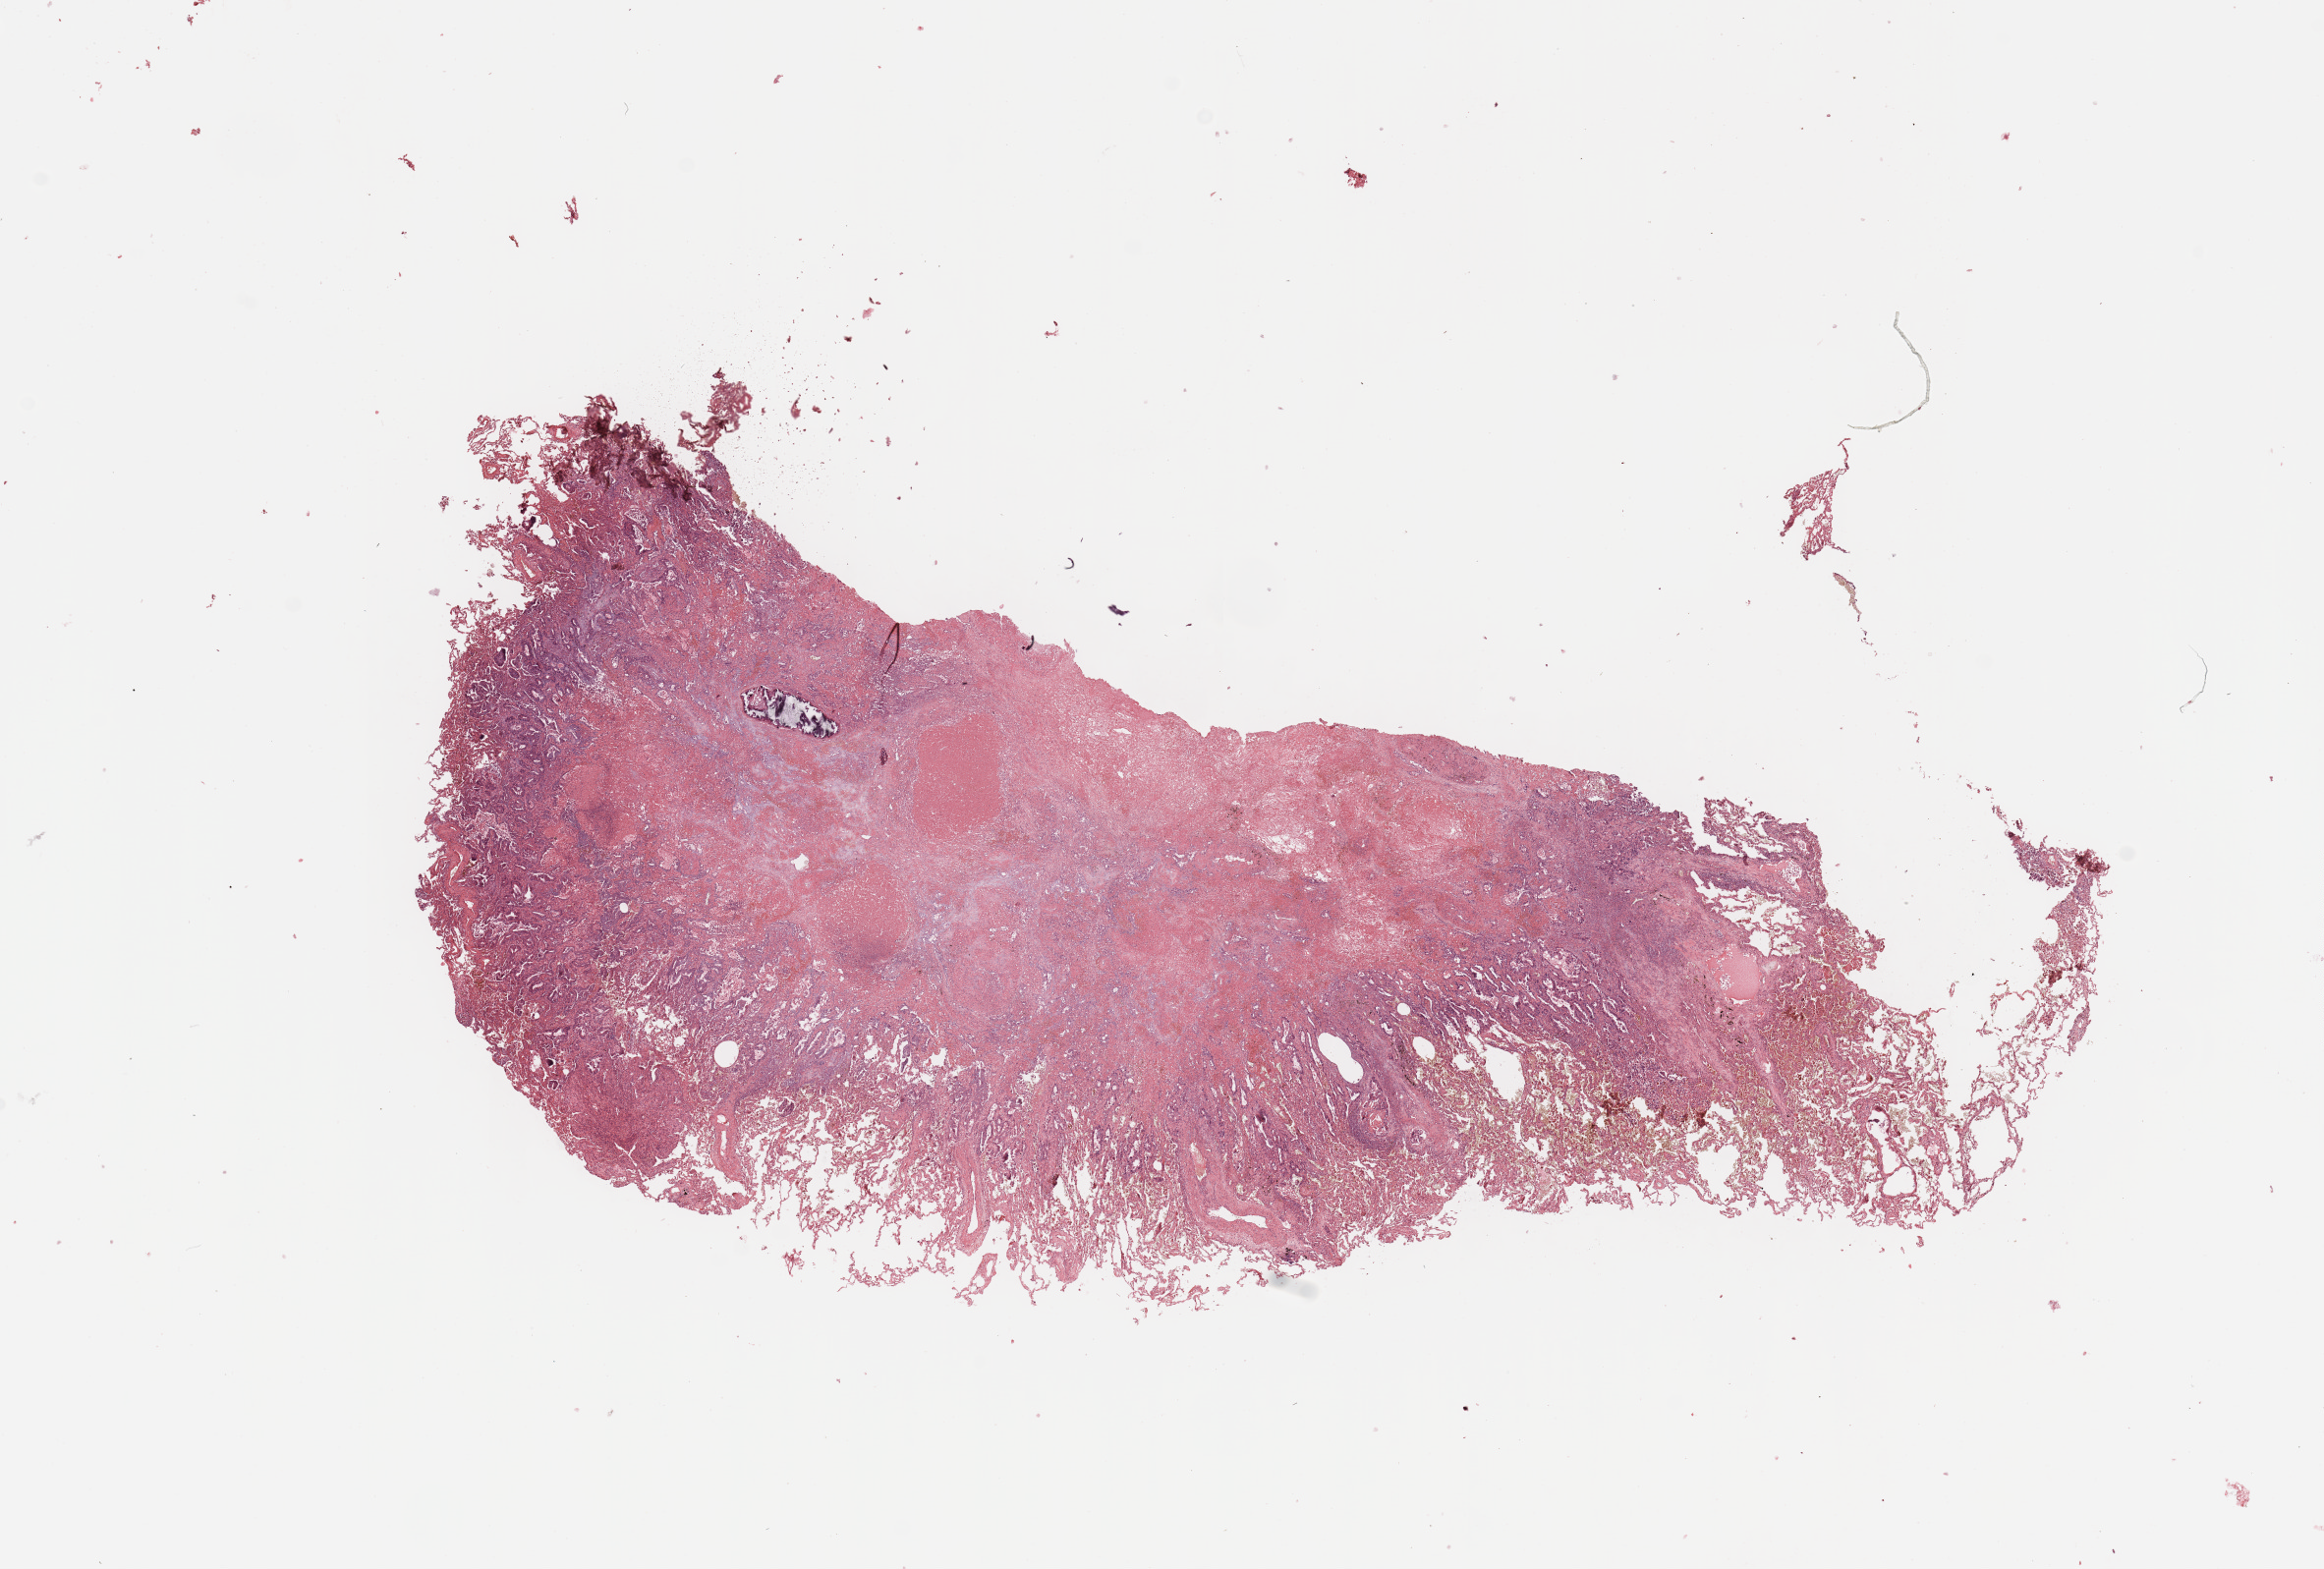
H&E-stained whole-slide image, shown as a low-resolution overview of the whole scanned area (about 18.7 x 12.6 mm, from a 20x scan). Tumour tissue sample, lung. Patient: male, age 69 years. Histologic grade: G2 (moderately differentiated).
• primary tumour site (as recorded): right lower lobe
• AJCC pathologic stage: IA
• histologic diagnosis: Adenocarcinoma, NOS